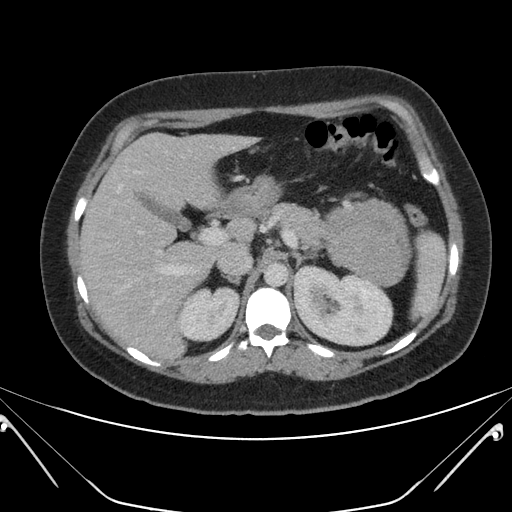
Contrast-enhanced abdominal CT, one axial slice. Position 129 of 168 along the scan axis. Soft-tissue window (W 400 / L 40 HU). 512 × 512 image matrix. Female patient, age 26 years. Case-level facts recorded for this patient, not image findings: diagnosis: adrenocortical carcinoma; tumour side: left adrenal; tumour size at pathology: 28 cm; Ki-67 index: 20 %; stage (as recorded): 2.
Structures marked on this image (semi-automatically segmented with operator editing):
- mass: box from (x=329, y=201) to (x=408, y=285) px